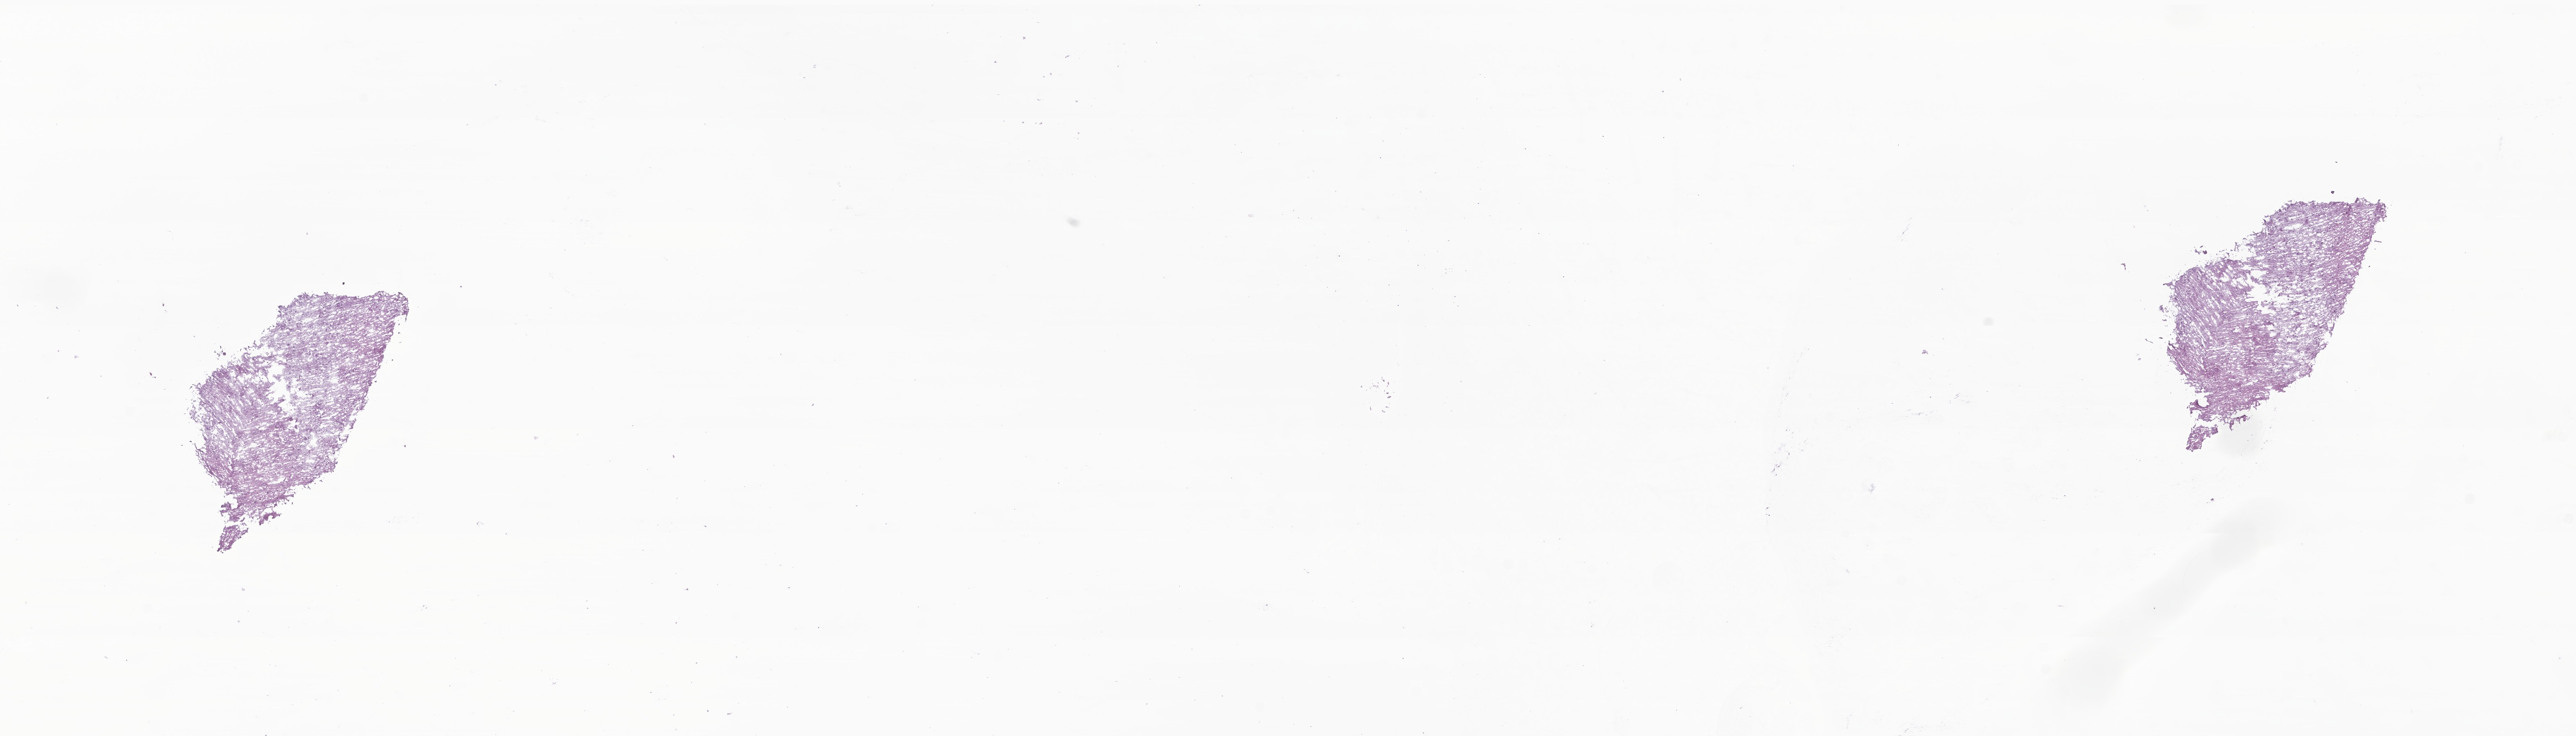
Digitized haematoxylin and eosin-stained section of tumor tissue from the brain, whole scanned area (about 26.5 x 7.6 mm) shown as a low-resolution overview. Frozen section (OCT-embedded). Patient: female, age 167 months.
Diagnosis: Ganglioglioma, NOS.